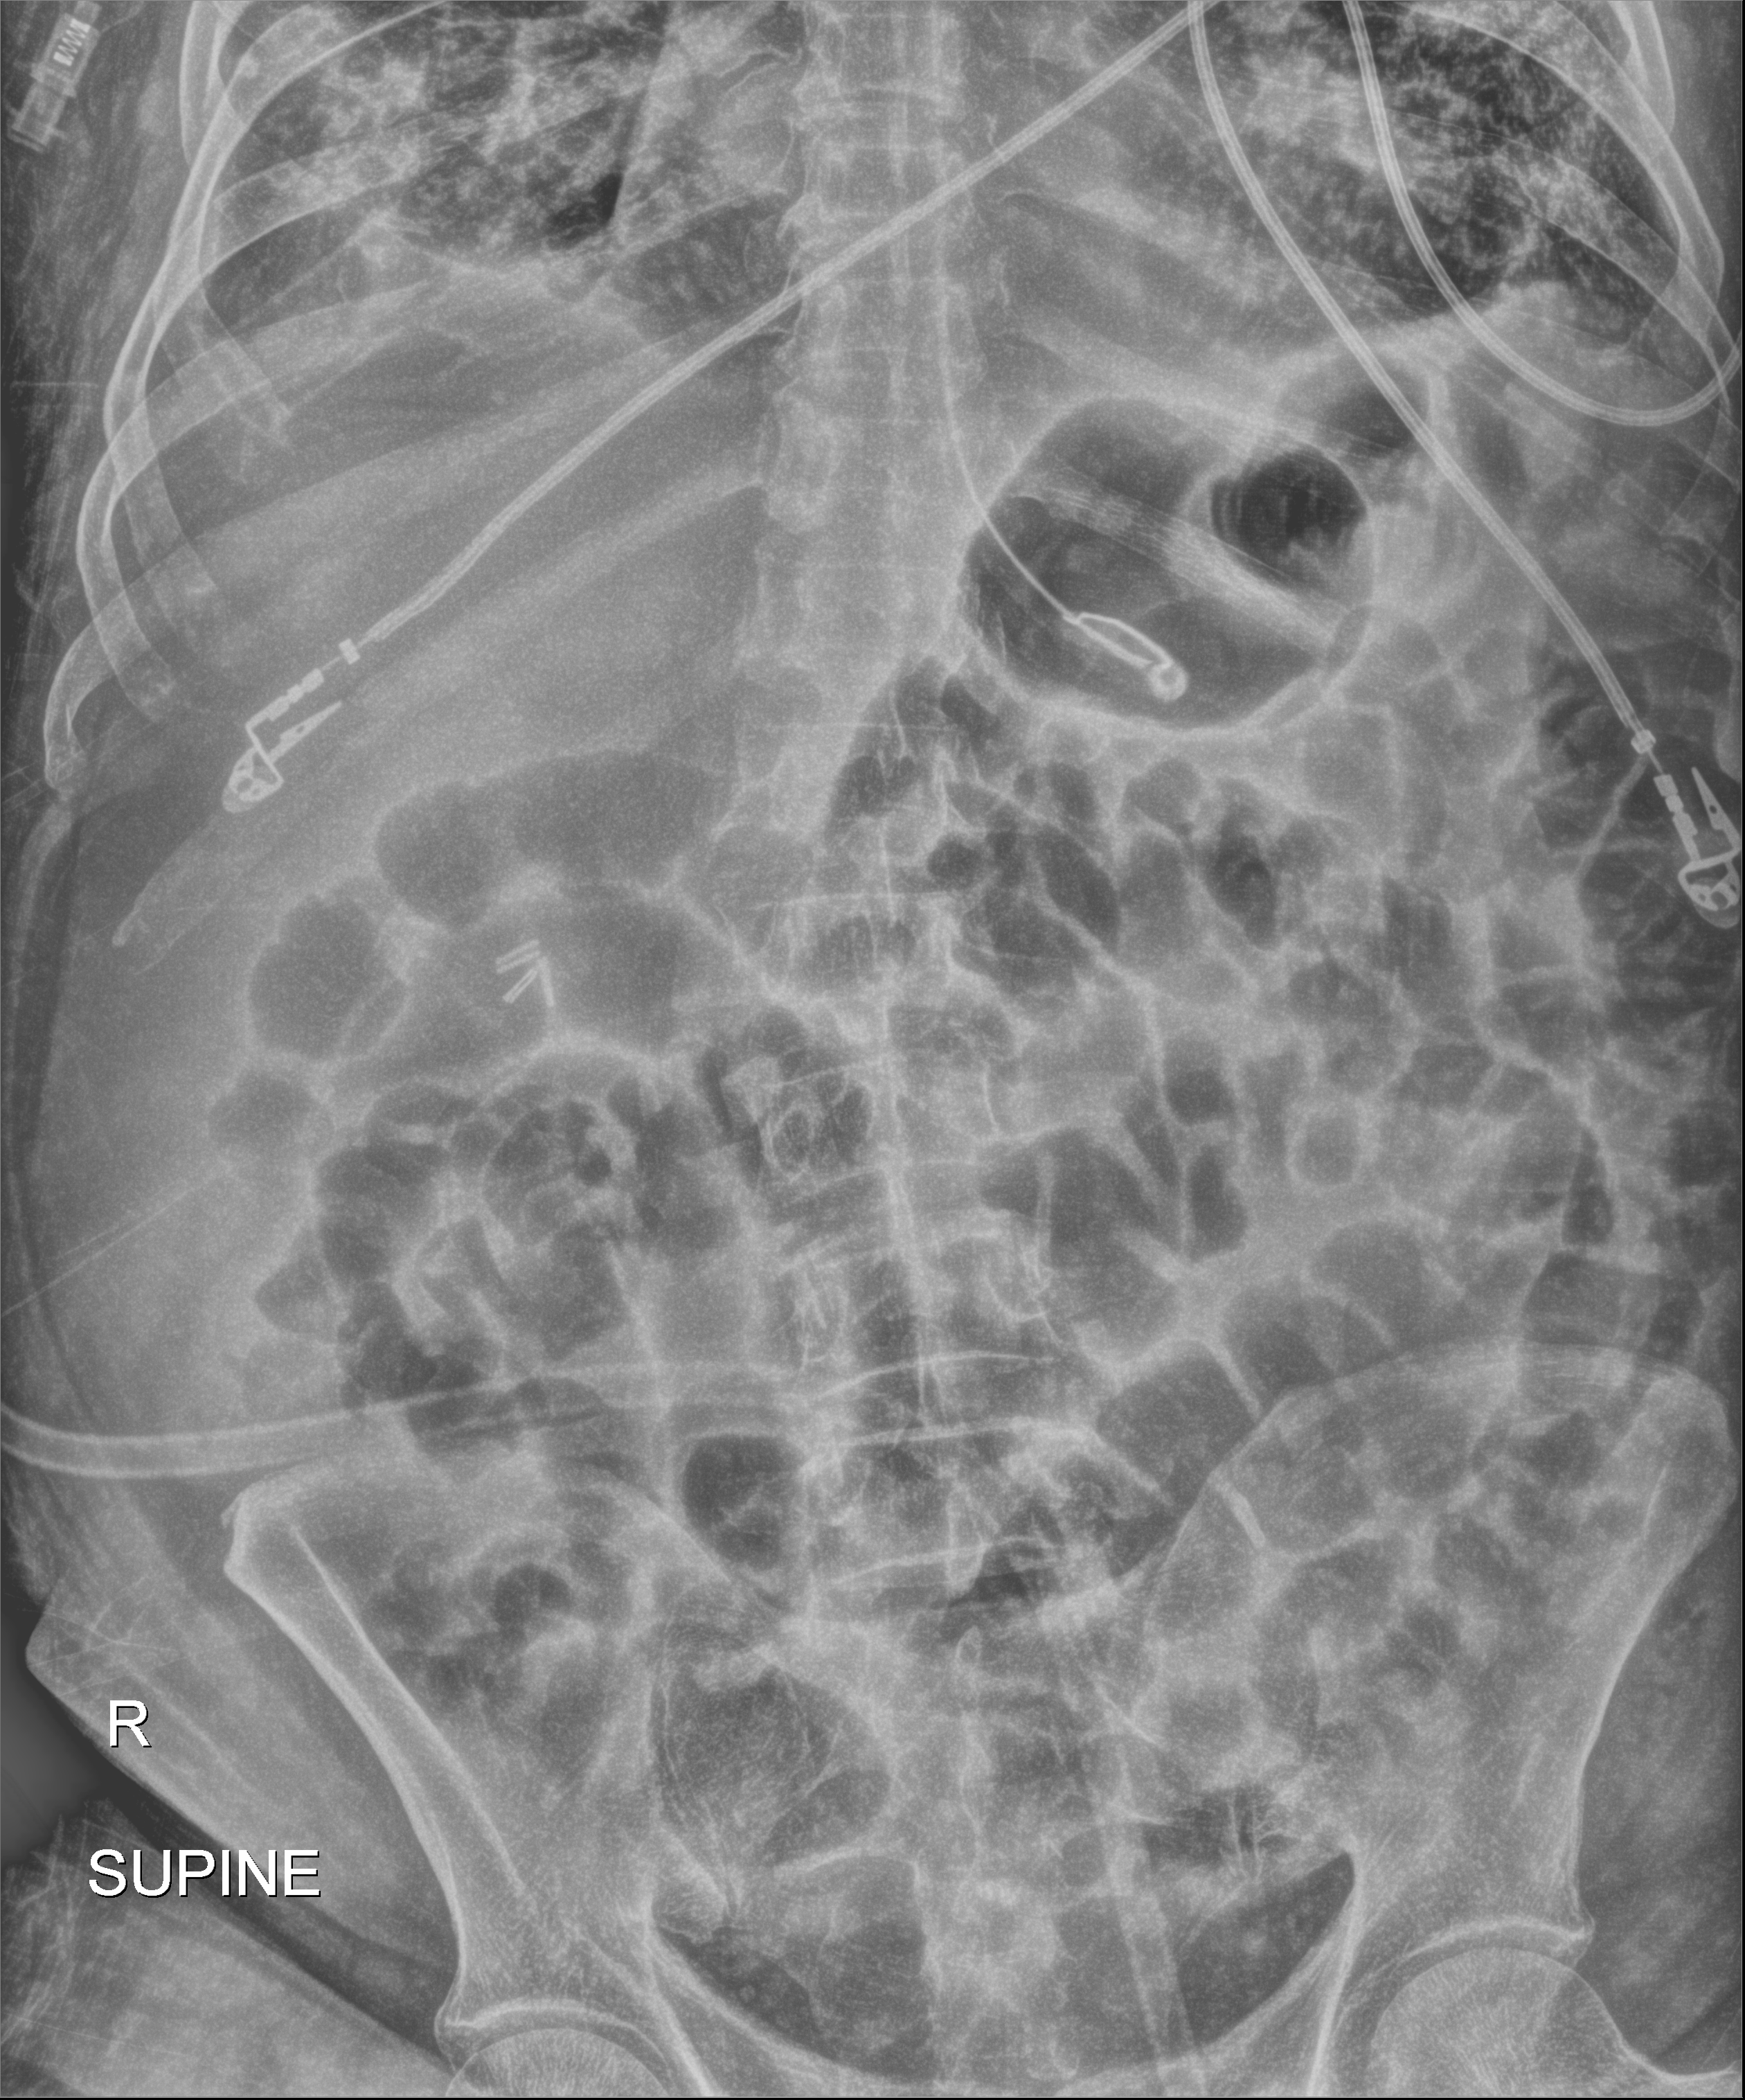
Bedside abdomen radiograph (digital radiography); anteroposterior (AP) projection. Male patient hospitalised with COVID-19, age 75–90 years.
Admission-level facts for this patient (not findings on this image; timing relative to this image not recorded): mechanically ventilated during this hospital stay: yes; admitted to intensive care during this hospital stay: yes.